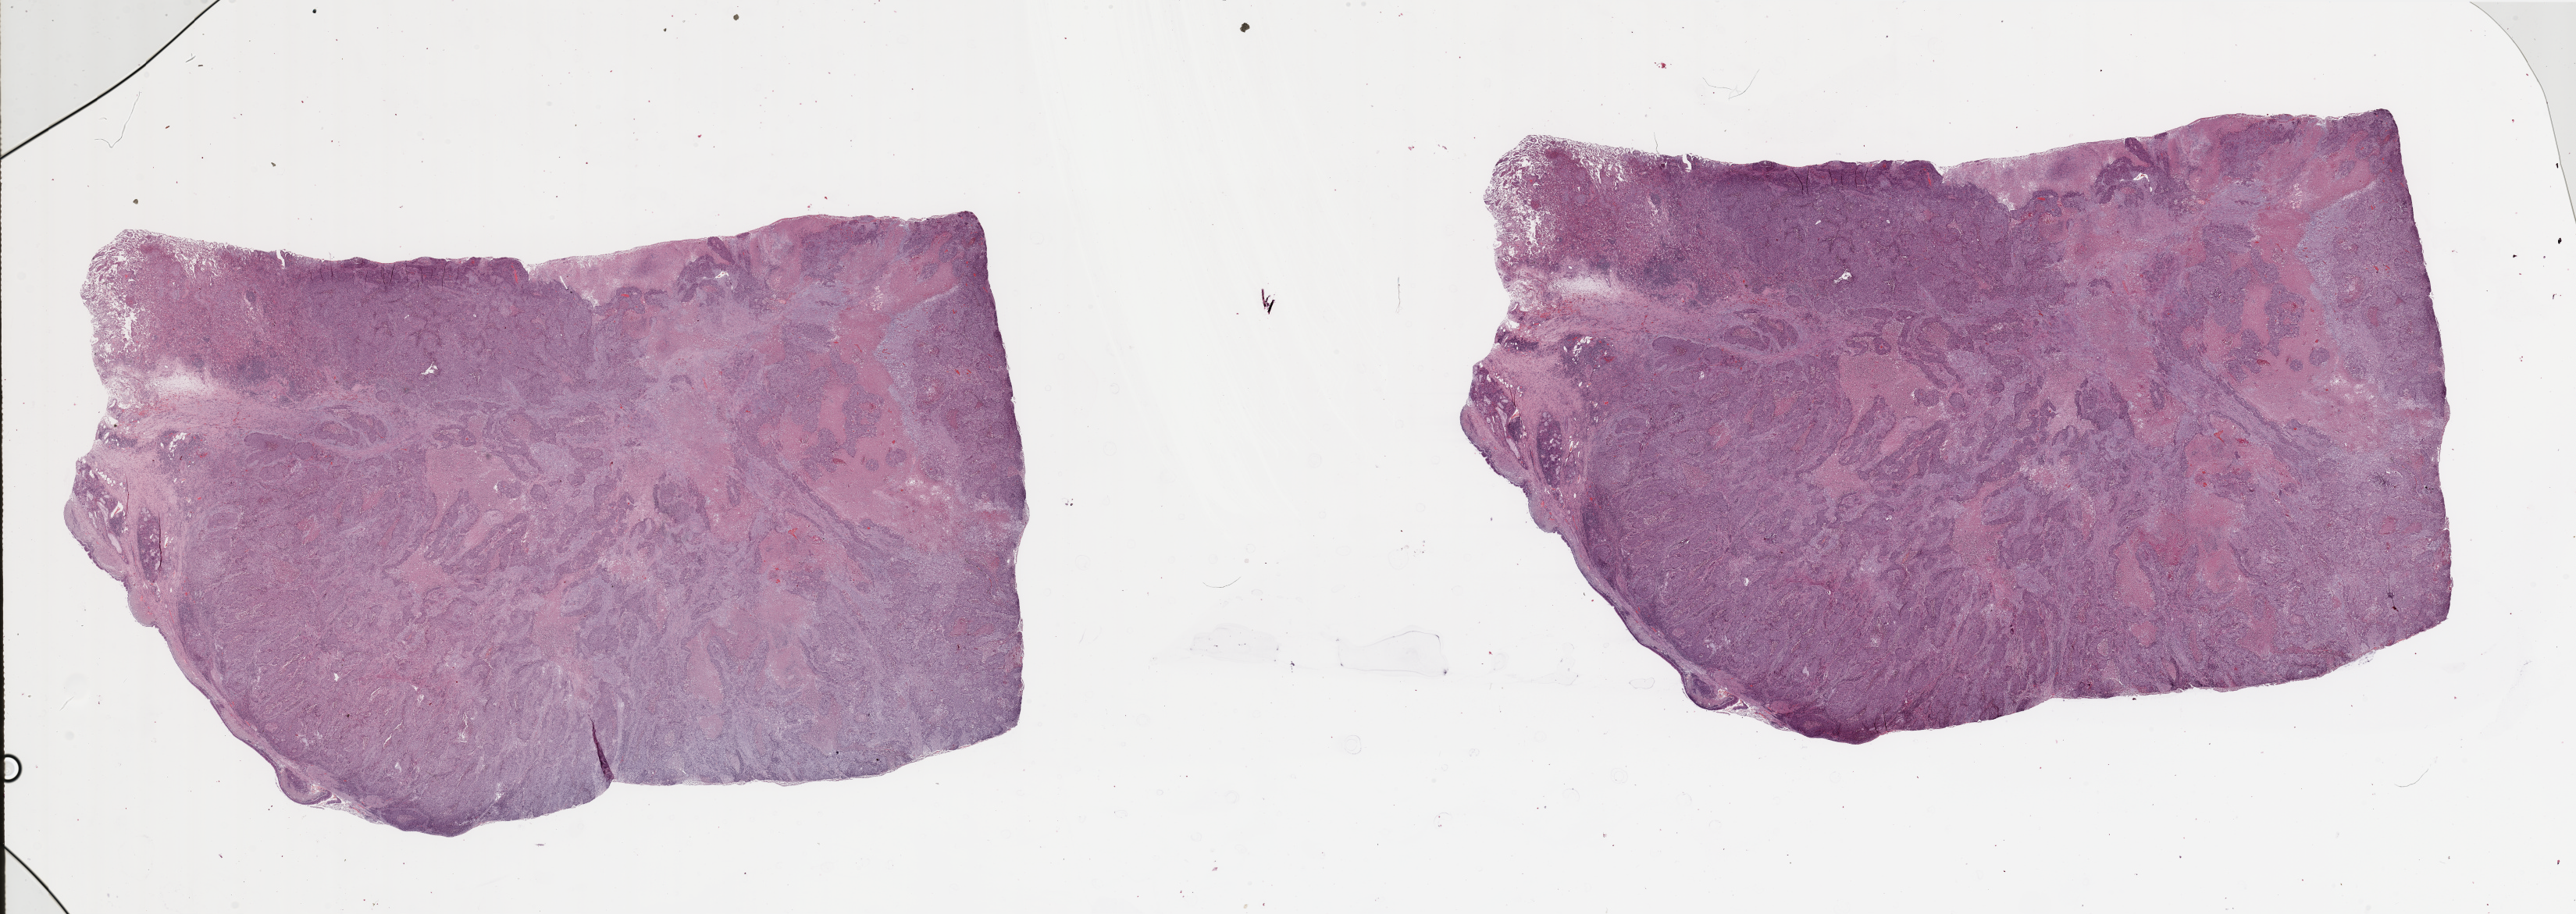
Whole-slide histology image, H&E — whole scanned area (about 52.2 x 18.5 mm, from a 20x scan) shown as a low-resolution overview; tumour tissue sample, sampled site: lung. 74-year-old male patient. Histologic grade: G2 (moderately differentiated). Slide review estimates, as recorded: tumour nuclei 75%, necrosis 20%.
• primary tumour site (as recorded): right middle lobe
• histologic diagnosis: Squamous cell carcinoma, NOS
• AJCC pathologic stage: IIA